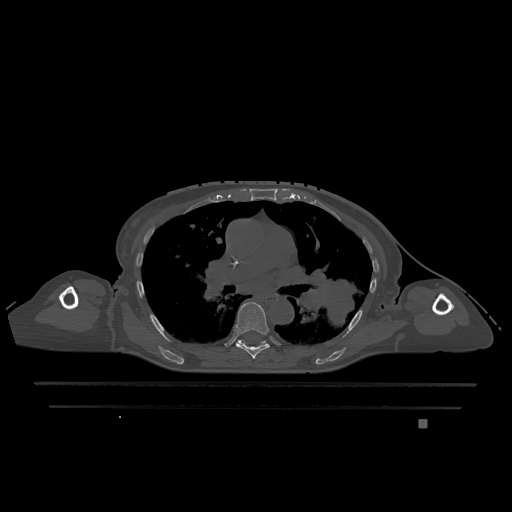
CT including the spine, one axial slice. Position 779 of 1317 along the scan axis. Bone window (W 1800 / L 400 HU). 0.5 mm slice thickness. 512 × 512 image matrix, field of view 500 × 500 mm. Patient: female, 74 years. From the clinical record (not read from this slice): primary cancer: lung; vertebrae with lytic lesions (as recorded): T1, T4, T5, T6, L4, L5.
Outlined on this slice (semi-automatically segmented with operator editing):
- T6 vertebra: box from (x=234, y=302) to (x=270, y=359) px
- T7 vertebra: (x=238, y=340)–(x=269, y=345)